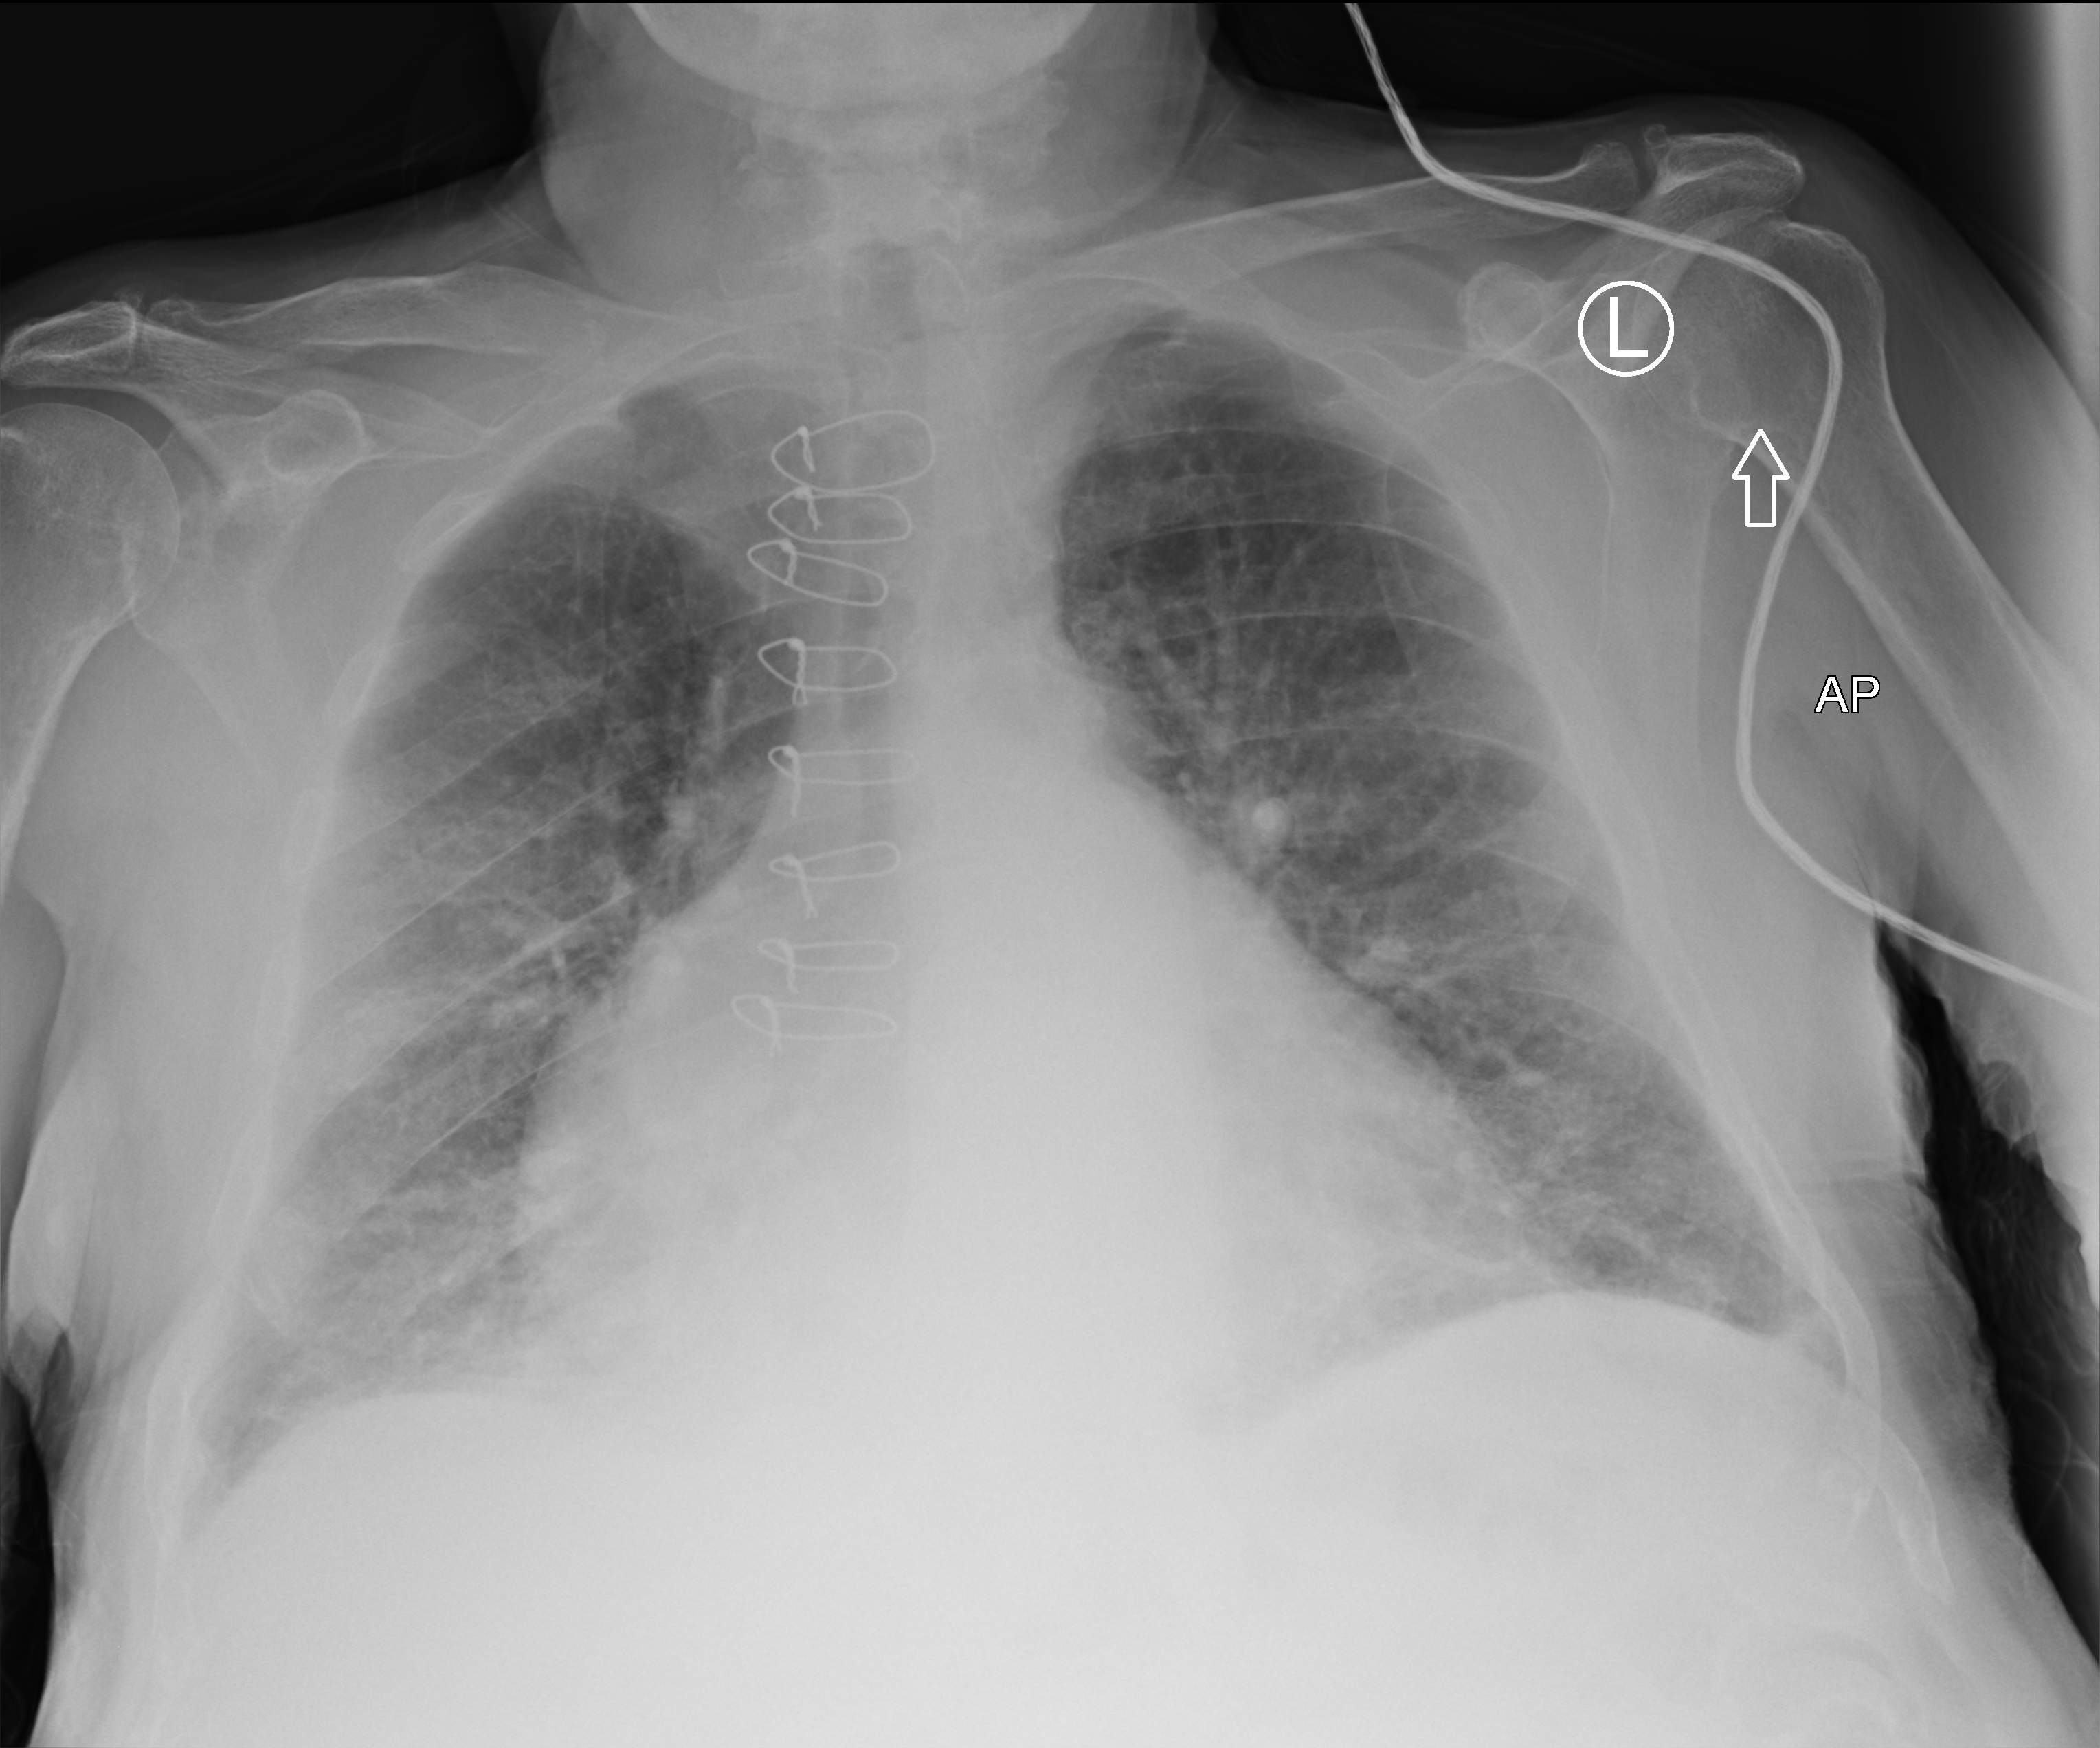
Chest radiograph (computed radiography), anteroposterior (AP) projection. Patient hospitalised with COVID-19; male, aged 75–90 years.
From the hospital-stay record, not from the radiograph (when in the stay this image was taken is not recorded): mechanically ventilated during this hospital stay: yes; admitted to intensive care during this hospital stay: yes.